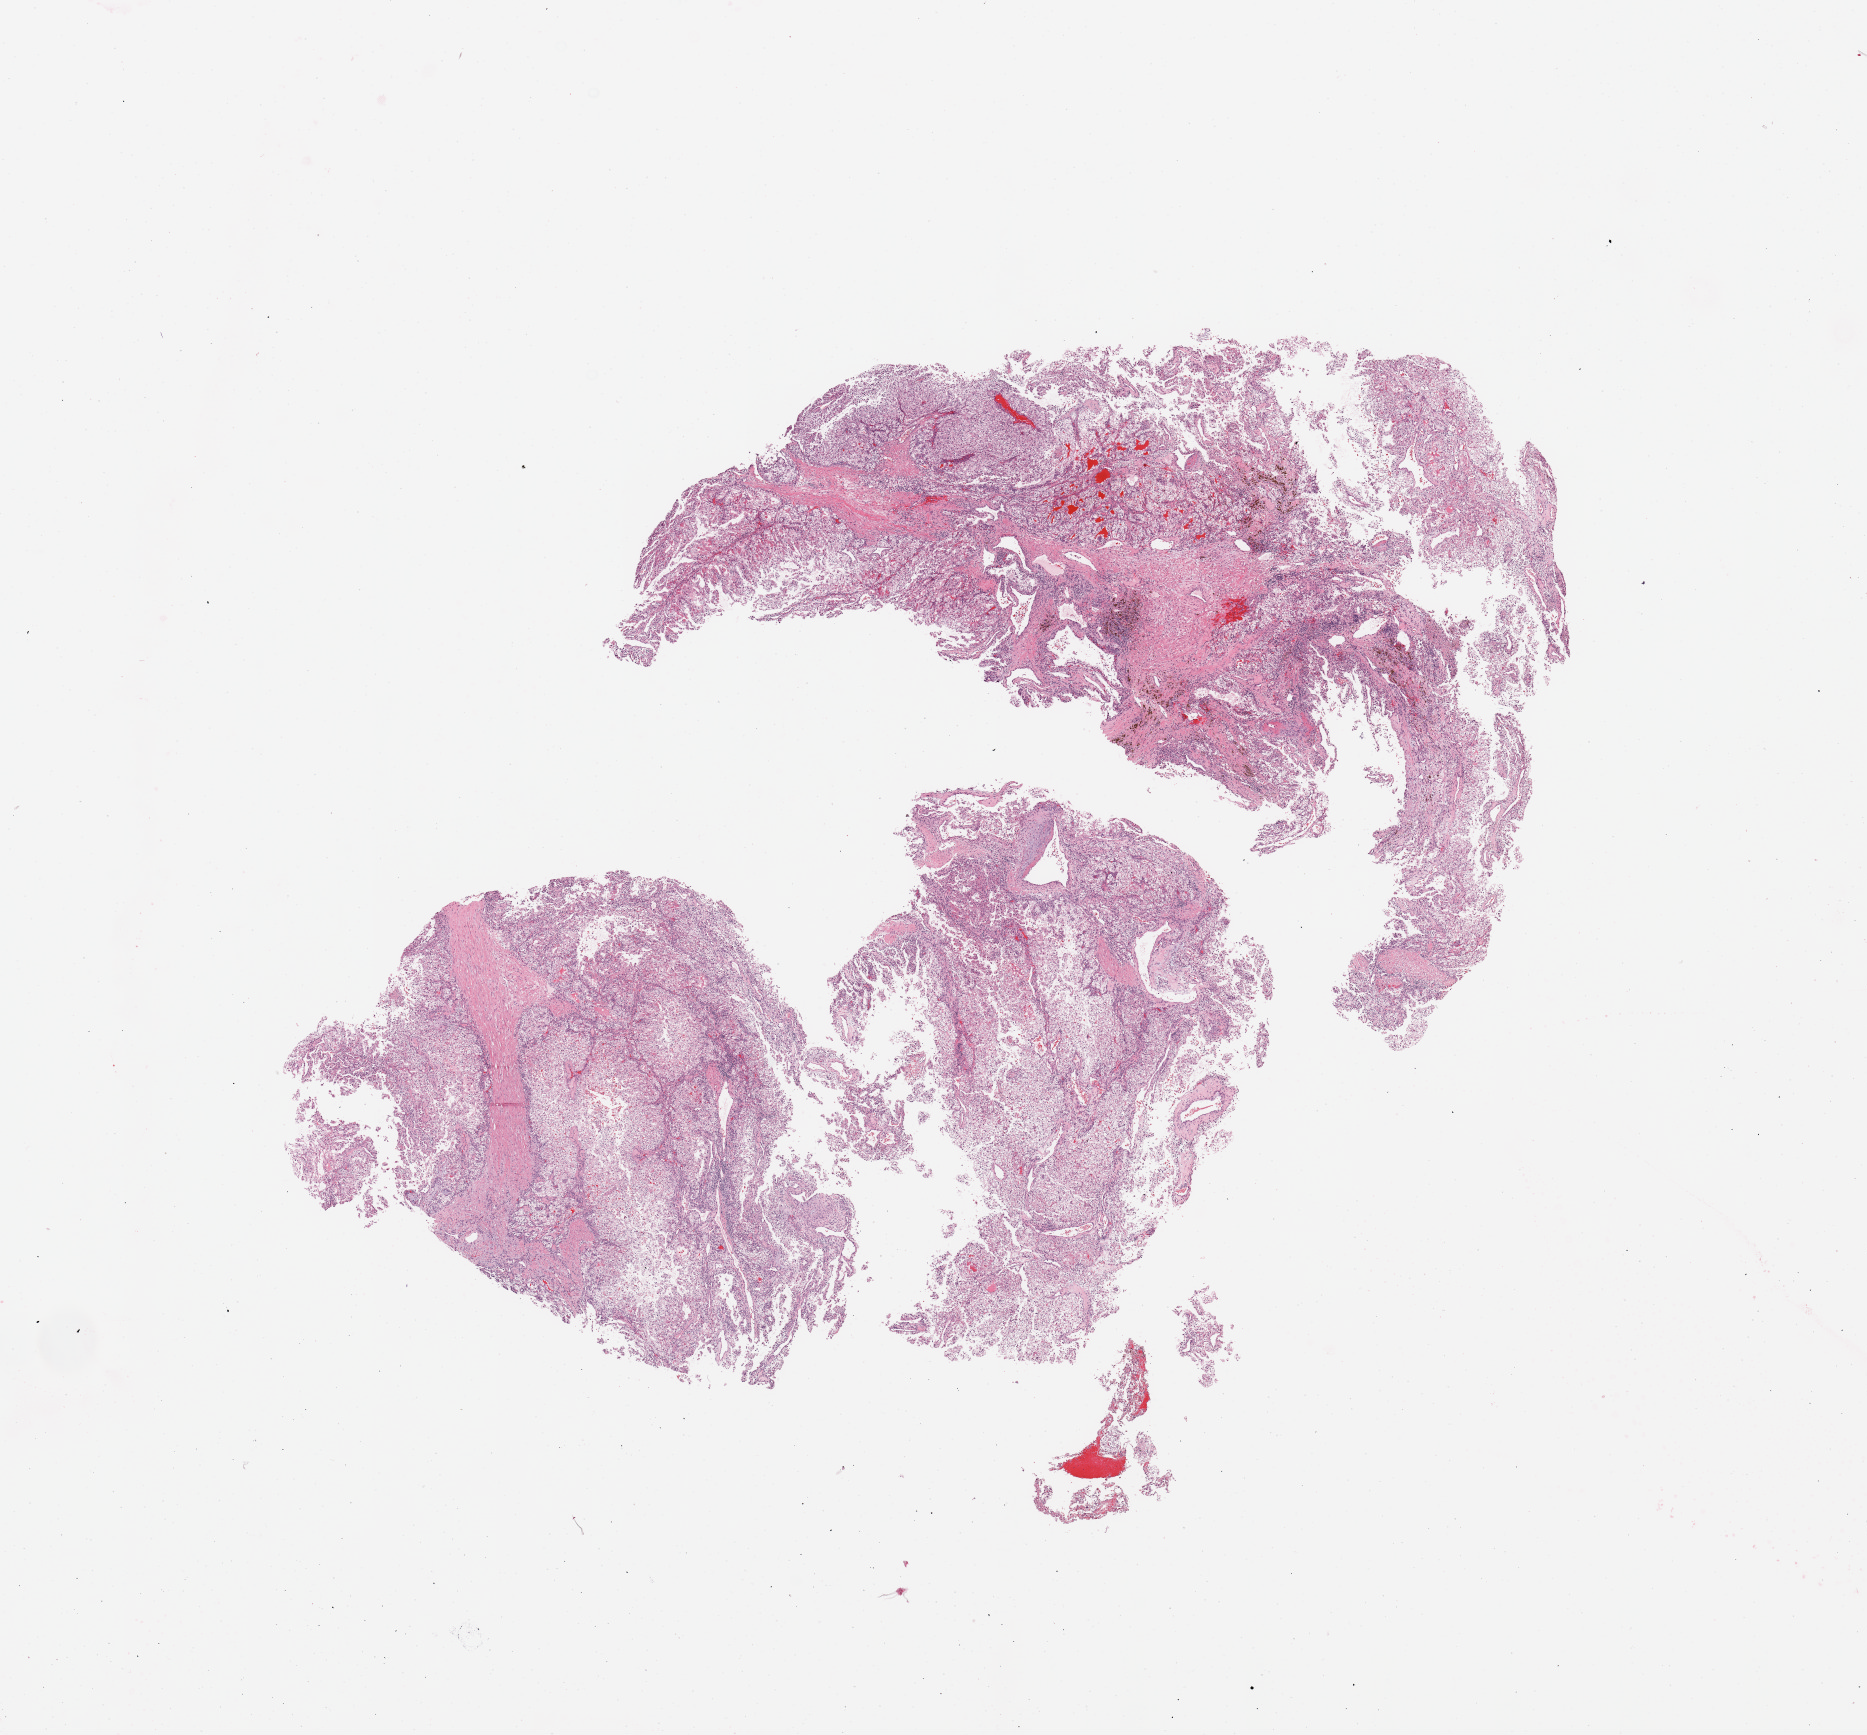
Whole-slide histology image, H&E — a low-resolution overview of the entire scanned area, about 14.8 x 13.7 mm (slide scanned at 20x); tumour tissue sample, sampled site: kidney. Patient: male, age 52 years. Histologic grade: G2 (moderately differentiated). Composition of this section per pathologist review: tumour nuclei 85%, necrosis 5%.
Histologic diagnosis: Renal cell carcinoma, NOS. AJCC pathologic stage: II.